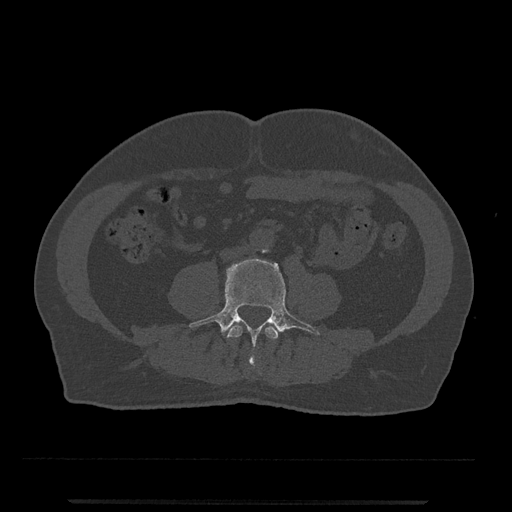
CT including the spine, one axial slice. Slice 151 of 797 in the series (ordered by position). Reconstruction kernel Br40s/3. 120 kVp. Bone window (W 1800 / L 400 HU). 512 × 512 image matrix, field of view 419 × 419 mm. Patient: male, 63 years. Case-level facts recorded for this patient, not image findings: primary cancer: prostate.
Structures marked on this image (semi-automatic segmentation, software-assisted and operator-edited):
- L3 vertebra: bounding box [x1, y1, x2, y2] px = [227, 324, 278, 368]
- L4 vertebra: [189, 258, 320, 365]